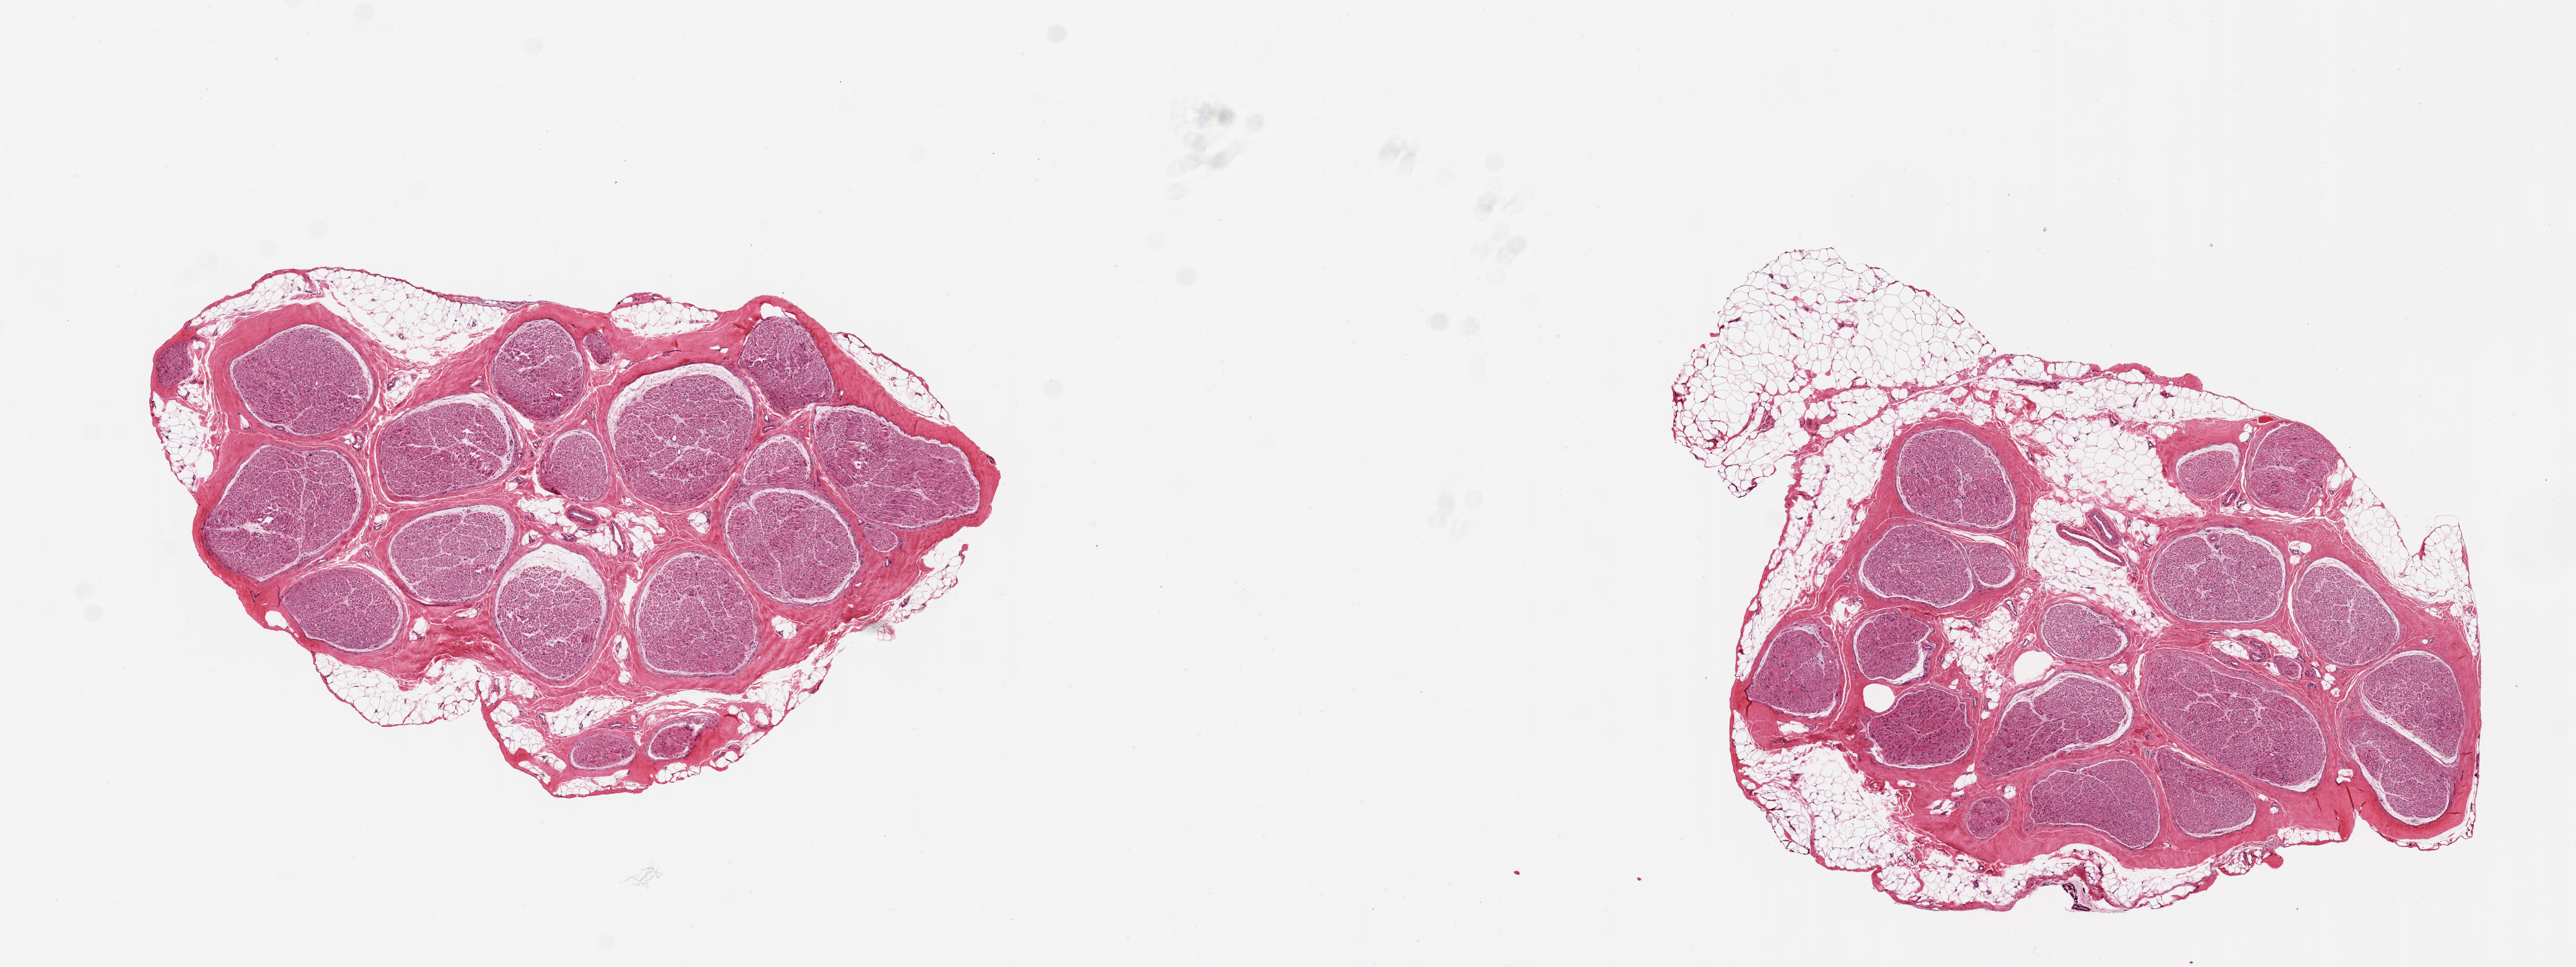
Digitized haematoxylin and eosin-stained section, shown as a low-resolution overview of the whole scanned area (about 14.8 x 5.5 mm). PAXgene-fixed paraffin-embedded (PFPE) section. Section of tibial nerve (target tissue). Tissue donor sample. Donor: male.
- review note (as recorded): 2 pieces ~4x3mm; Discontinuous adherent fat up to ~1mm